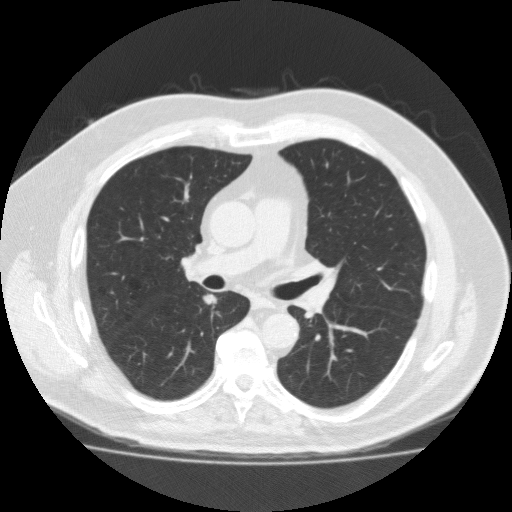
Low-dose screening chest CT, one axial slice; slice 112 of 183 in the series (ordered by position); reconstruction kernel FC10; 120 kVp; lung window (W 1500 / L -600 HU); 512 × 512 image matrix, field of view 391 × 391 mm.
Outlined on this slice (outlined manually by an expert reader):
- lesion 1 (tumor, lower lobe of right lung): box from (x=204, y=295) to (x=216, y=304) px